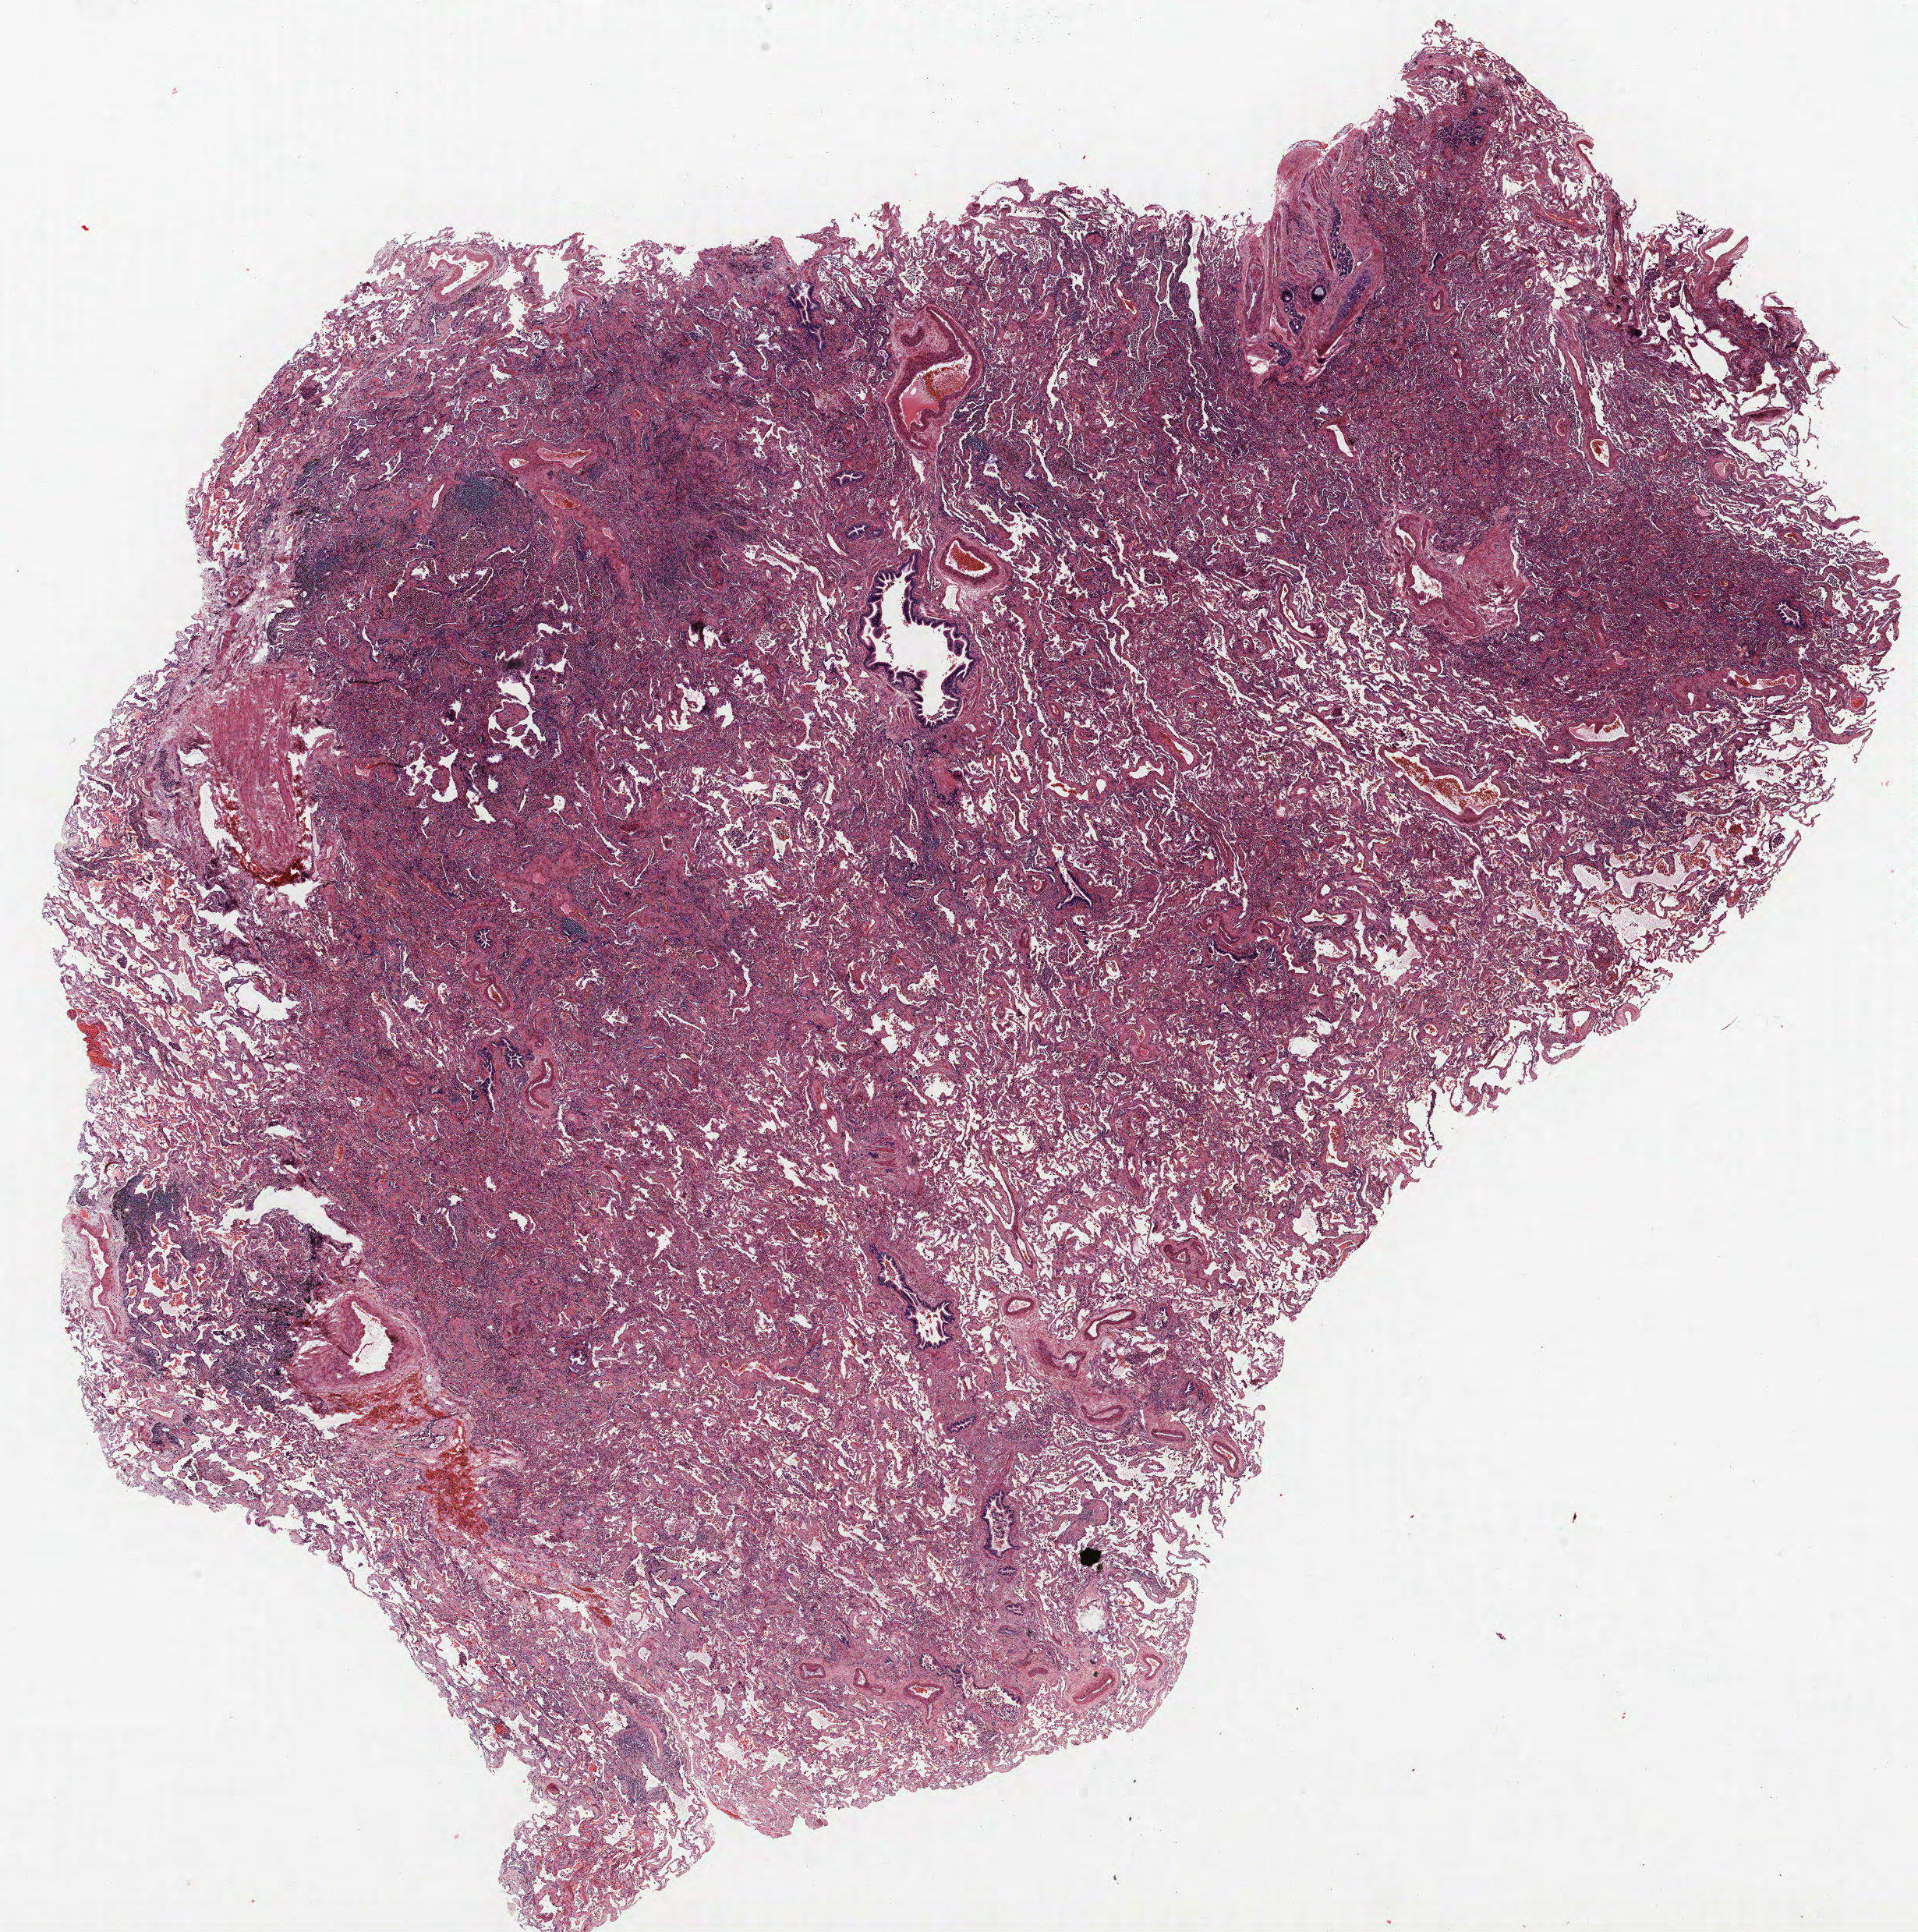
H&E-stained whole-slide image, a low-resolution overview of the entire scanned area, about 19.7 x 19.8 mm (slide scanned at 40x). FFPE section. Lung. Female, age 55 at enrolment. Current smoker at enrolment. Grade: moderately differentiated (G2).
* stage (AJCC 6th edition): IA
* participant's lung-cancer diagnosis: Bronchiolo-alveolar adenocarcinoma, NOS (ICD-O-3 8250/3)
* primary tumour location (clinical record): right lower lobe
* tumour size (pathology): 12 mm